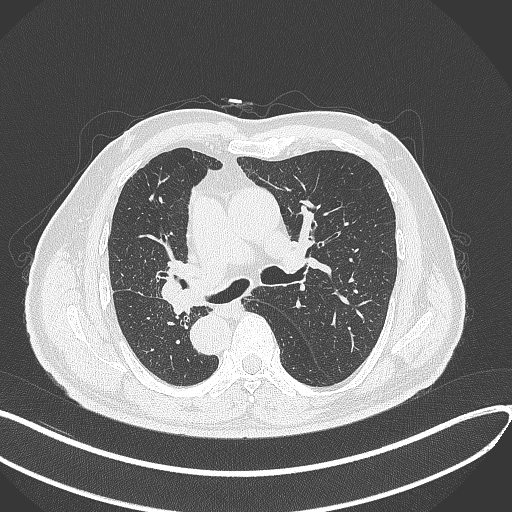
Chest CT, one axial slice; position 177 of 300 along the scan axis; lung window (W 1500 / L -600 HU); 1 mm slice thickness; 512 × 512 image matrix. Male patient, age 67 years. From the clinical record (not read from this slice): clinical TNM (as recorded): T2a N0 M0.
Outlined on this slice (rectangle marked by the reading radiologist):
- lung tumour (recorded histology: squamous cell carcinoma): bounding box <154,259,198,314> (left, top, right, bottom; pixels)